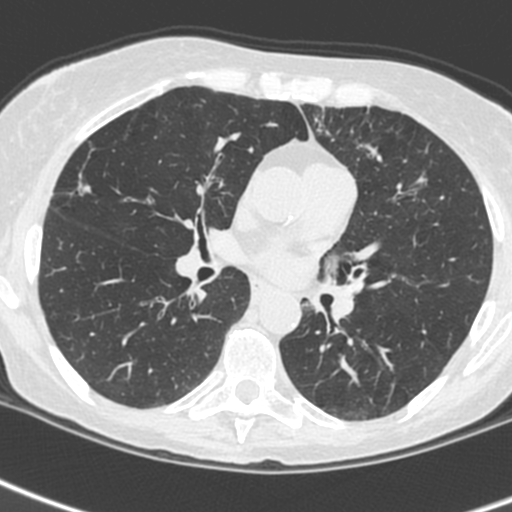
Low-dose screening chest CT, one axial slice. Position 134 of 242 along the scan axis. Lung window (W 1500 / L -600 HU). 1.3 mm slice thickness. 512 × 512 image matrix.
Annotated regions visible in this slice (outlined manually by an expert reader):
- lesion 3 (tumor, upper lobe of left lung): bounding box [x1, y1, x2, y2] px = [310, 255, 353, 320]